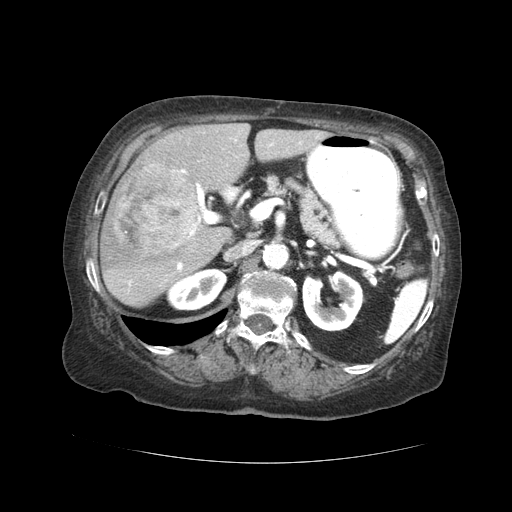
Contrast-enhanced abdominal CT (liver protocol), one axial slice; slice 18 of 59 in the series (ordered by position); soft-tissue window (W 400 / L 40 HU); 2.5 mm slice thickness; 512 × 512 image matrix, field of view 380 × 380 mm. From the clinical record (not read from this slice): diagnosis: hepatocellular carcinoma (patient treated with transarterial chemoembolisation; whether this scan precedes or follows treatment is not stated here); TNM stage (as recorded): Stage-I; Child-Pugh class: A; tumour nodularity: uninodular.
Outlined on this slice (semi-automatic segmentation, software-assisted and operator-edited):
- liver parenchyma outside the tumour (the mass and vessels are separate outlines, so this box may not span the whole liver): bounding box <100,124,326,308> (left, top, right, bottom; pixels)
- mass: <109,168,200,252>
- liver vessels: <128,136,319,286>